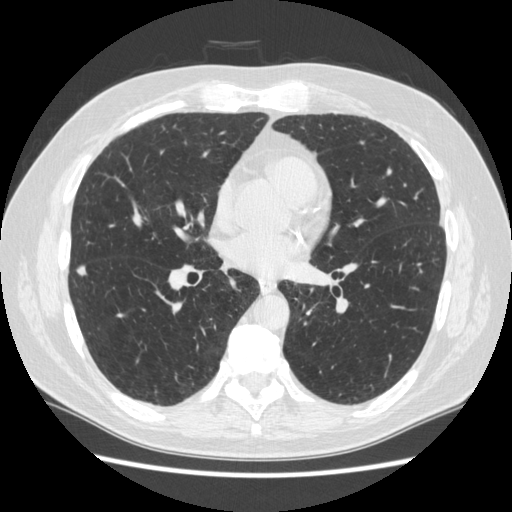
Low-dose screening chest CT, one axial slice; position 125 of 267 along the scan axis; 120 kVp; lung window (W 1500 / L -600 HU); 1.25 mm slice thickness; 512 × 512 image matrix.
Structures marked on this image (outlined manually by an expert reader):
- lesion 2 (nodule, lower lobe of right lung): box from (x=77, y=265) to (x=88, y=276) px